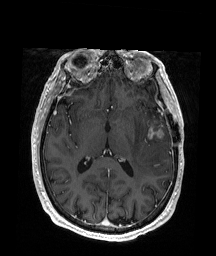
Brain MRI from a brain-tumour surgery series, one axial slice; slice 94 of 176 in the series (ordered by position); T1-weighted post-contrast; 216 × 256 image matrix, field of view 219 × 260 mm. Case-level facts recorded for this patient, not image findings: histopathology: Glioblastoma; WHO grade: 4; IDH mutation: no; tumour location: Left Frontal.
Structures marked on this image (manually delineated by an expert):
- tumour: box from (x=148, y=116) to (x=165, y=139) px